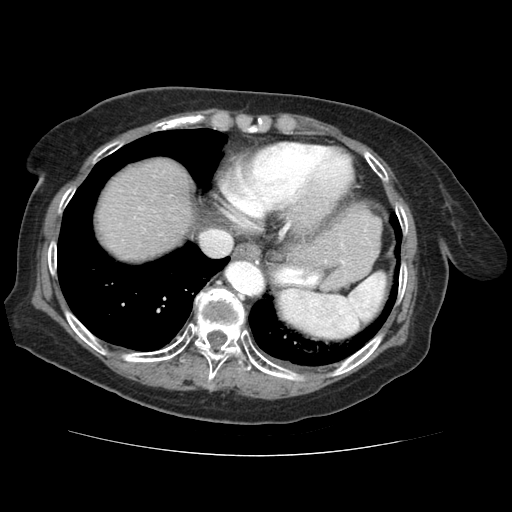
Contrast-enhanced abdominal CT (liver protocol), one axial slice; reconstruction kernel STANDARD; 120 kVp; soft-tissue window (W 400 / L 40 HU); 2.5 mm slice thickness; 512 × 512 image matrix. From the clinical record (not read from this slice): diagnosis: hepatocellular carcinoma (patient treated with transarterial chemoembolisation; whether this scan precedes or follows treatment is not stated here); TNM stage (as recorded): Stage-IVB; Child-Pugh class: A.
Outlined on this slice (semi-automatically segmented with operator editing):
- liver parenchyma outside the tumour (the mass and vessels are separate outlines, so this box may not span the whole liver): bounding box (x1, y1, x2, y2) in pixels: (98, 158, 192, 260)